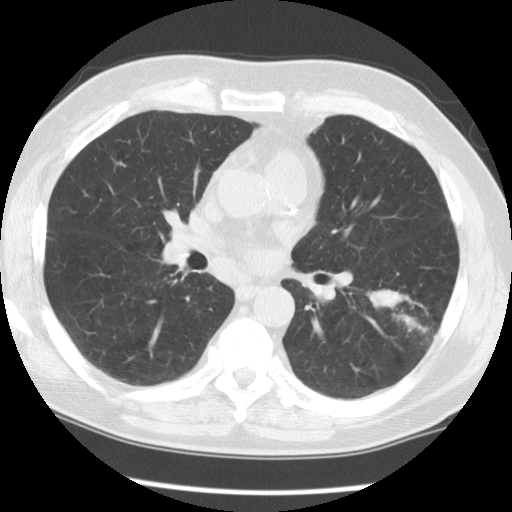
Axial slice from a low-dose chest CT screening exam; baseline annual screen; lung window (W 1500 / L -600 HU); 2.5 mm slice thickness; 512 × 512 image matrix. Male, age 71 years at enrolment. Former smoker at enrolment.
Expert-annotated lung lesion, bounding box (x1, y1, x2, y2) in pixels: (369, 271, 462, 364). The screening reader recorded 3 non-calcified nodules or masses ≥4 mm on this exam (left lower lobe, right upper lobe, right upper lobe); which of them this box marks is not recorded. Official screen result: positive, change unspecified: nodule(s) >= 4 mm or enlarging nodule(s), mass(es), or other non-specific abnormalities suspicious for lung cancer.